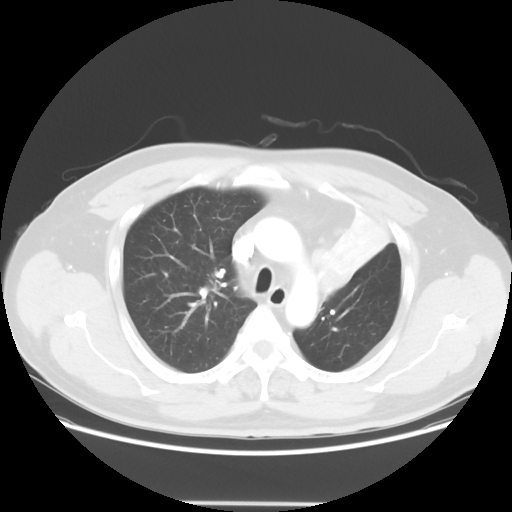
Chest CT, one axial slice. Slice 44 of 62 in the series (ordered by position). Reconstruction kernel STANDARD. Lung window (W 1500 / L -600 HU). 5 mm slice thickness. 512 × 512 image matrix, field of view 403 × 403 mm. Patient: male, 49 years. Case-level facts recorded for this patient, not image findings: clinical TNM (as recorded): T3 N3 M1c.
Structures marked on this image (rectangle marked by the reading radiologist):
- lung tumour (recorded histology: squamous cell carcinoma): bounding box [x1, y1, x2, y2] px = [307, 246, 361, 314]